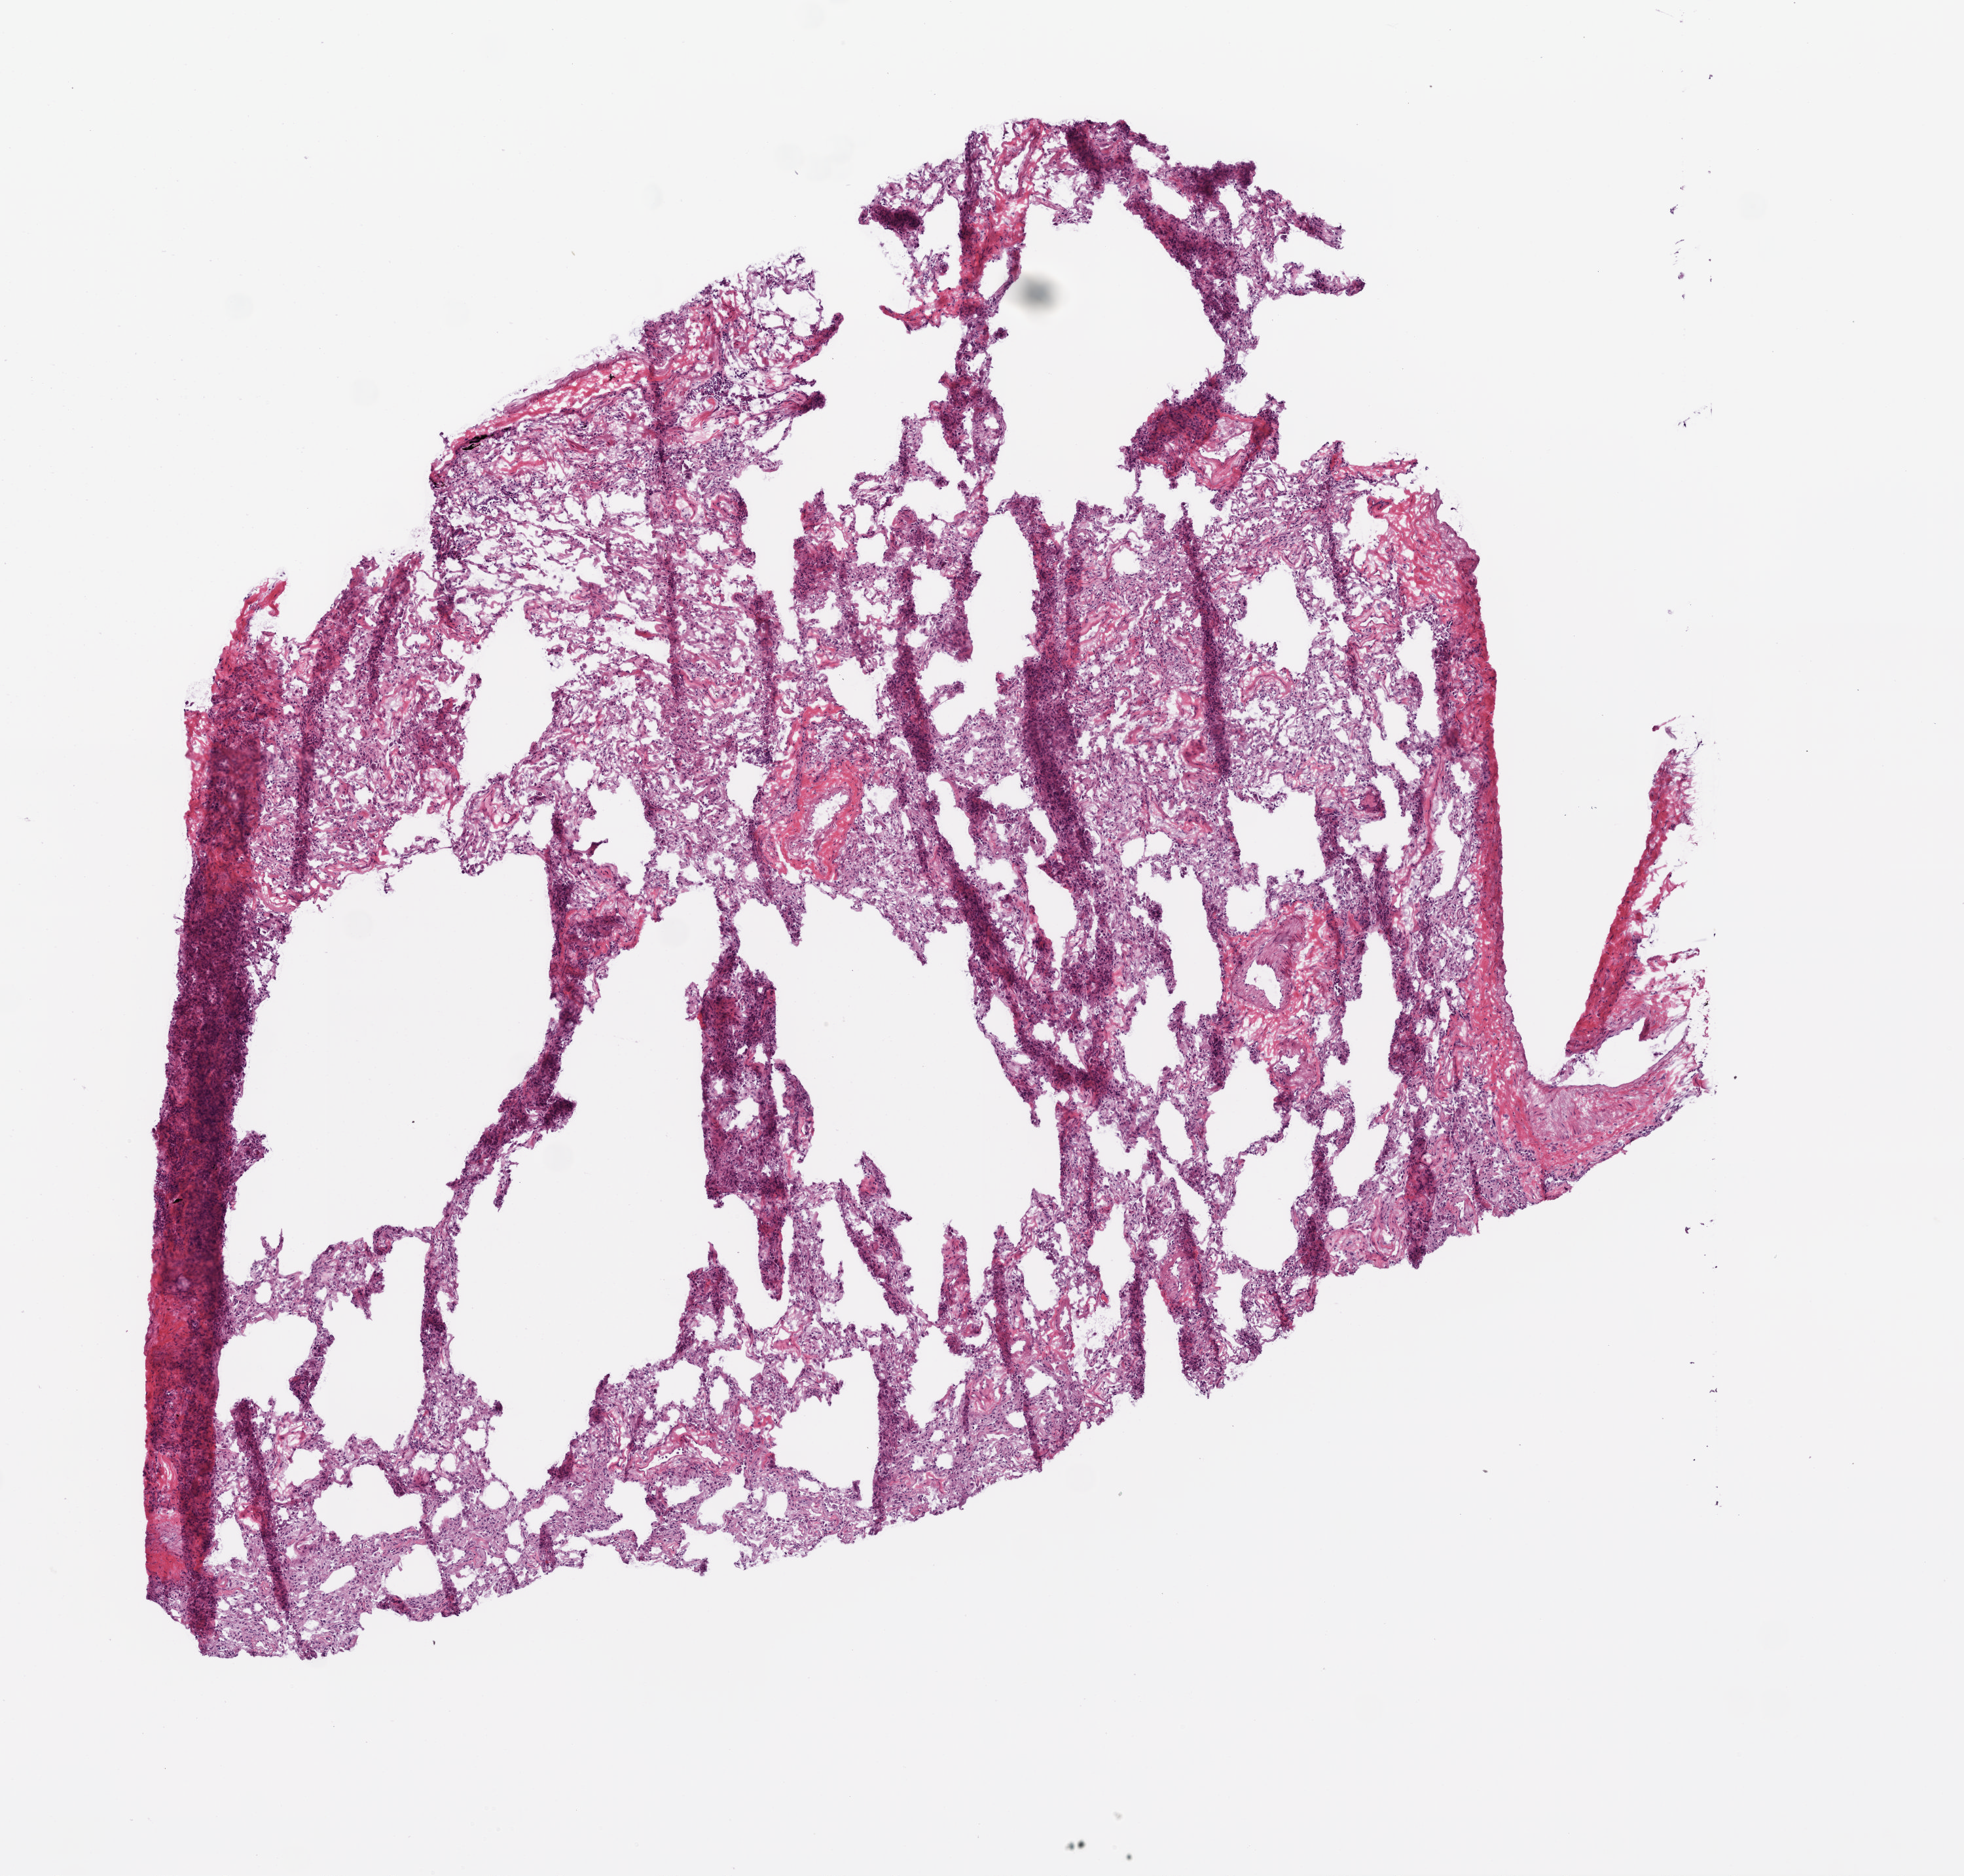
Hematoxylin and eosin (H&E) stained whole-slide image, whole scanned area (about 6.0 x 5.7 mm, acquisition: 20x scan) shown as a low-resolution overview; frozen section from the top of the tissue portion; lung, solid tissue normal (non-tumour tissue) sample. Patient: male, age at initial diagnosis 63 years.
* this section: solid tissue normal sample (biorepository sample class)
* patient diagnosis: Squamous cell carcinoma, NOS (lower lobe, lung)